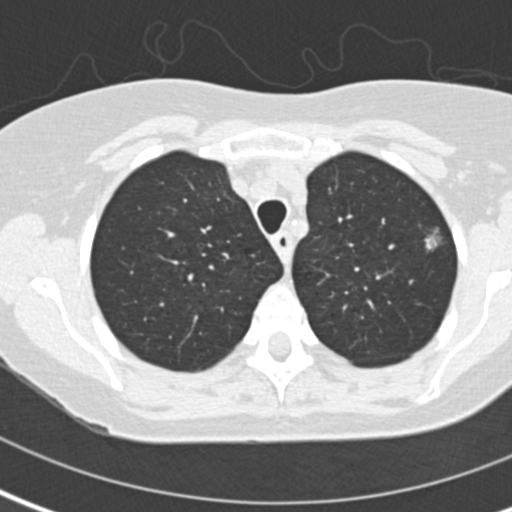
Axial slice from a low-dose chest CT screening exam, second annual screen, lung window (W 1500 / L -600 HU), standard (soft-tissue) reconstruction kernel (B30f), slice 29 of 141 in the series. Female, age 60 years at enrolment. Former smoker at enrolment.
• Expert-annotated lung lesion, bounding box <413,223,465,263> (left, top, right, bottom; pixels).
• The screening reader recorded 2 non-calcified nodules or masses ≥4 mm on this exam (left upper lobe, left upper lobe); which of them this box marks is not recorded.
• Lung cancer was diagnosed 116 days after this screen: adenocarcinoma, NOS, left upper lobe, moderately differentiated (G2), stage IA (AJCC 6th edition), 11 mm at pathology.